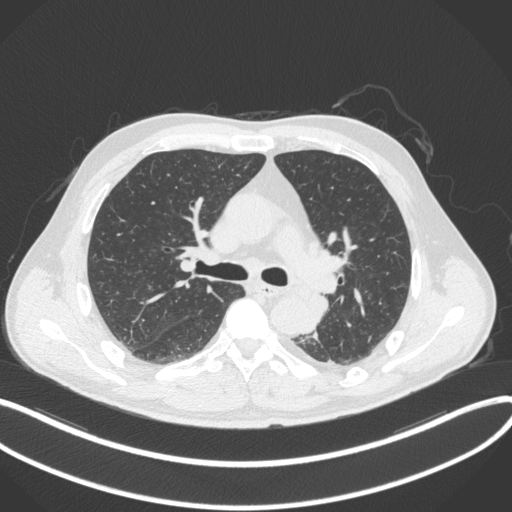
Chest CT, one axial slice; slice 218 of 328 in the series (ordered by position); reconstruction kernel B31f; lung window (W 1500 / L -600 HU); 1 mm slice thickness; 512 × 512 image matrix, field of view 400 × 400 mm. Male patient, age 59 years. Case-level facts recorded for this patient, not image findings: clinical TNM (as recorded): T2a N2 M0.
Structures marked on this image (bounding box drawn by a radiologist):
- lung tumour (recorded histology: squamous cell carcinoma): bounding box (x1, y1, x2, y2) in pixels: (306, 292, 332, 325)